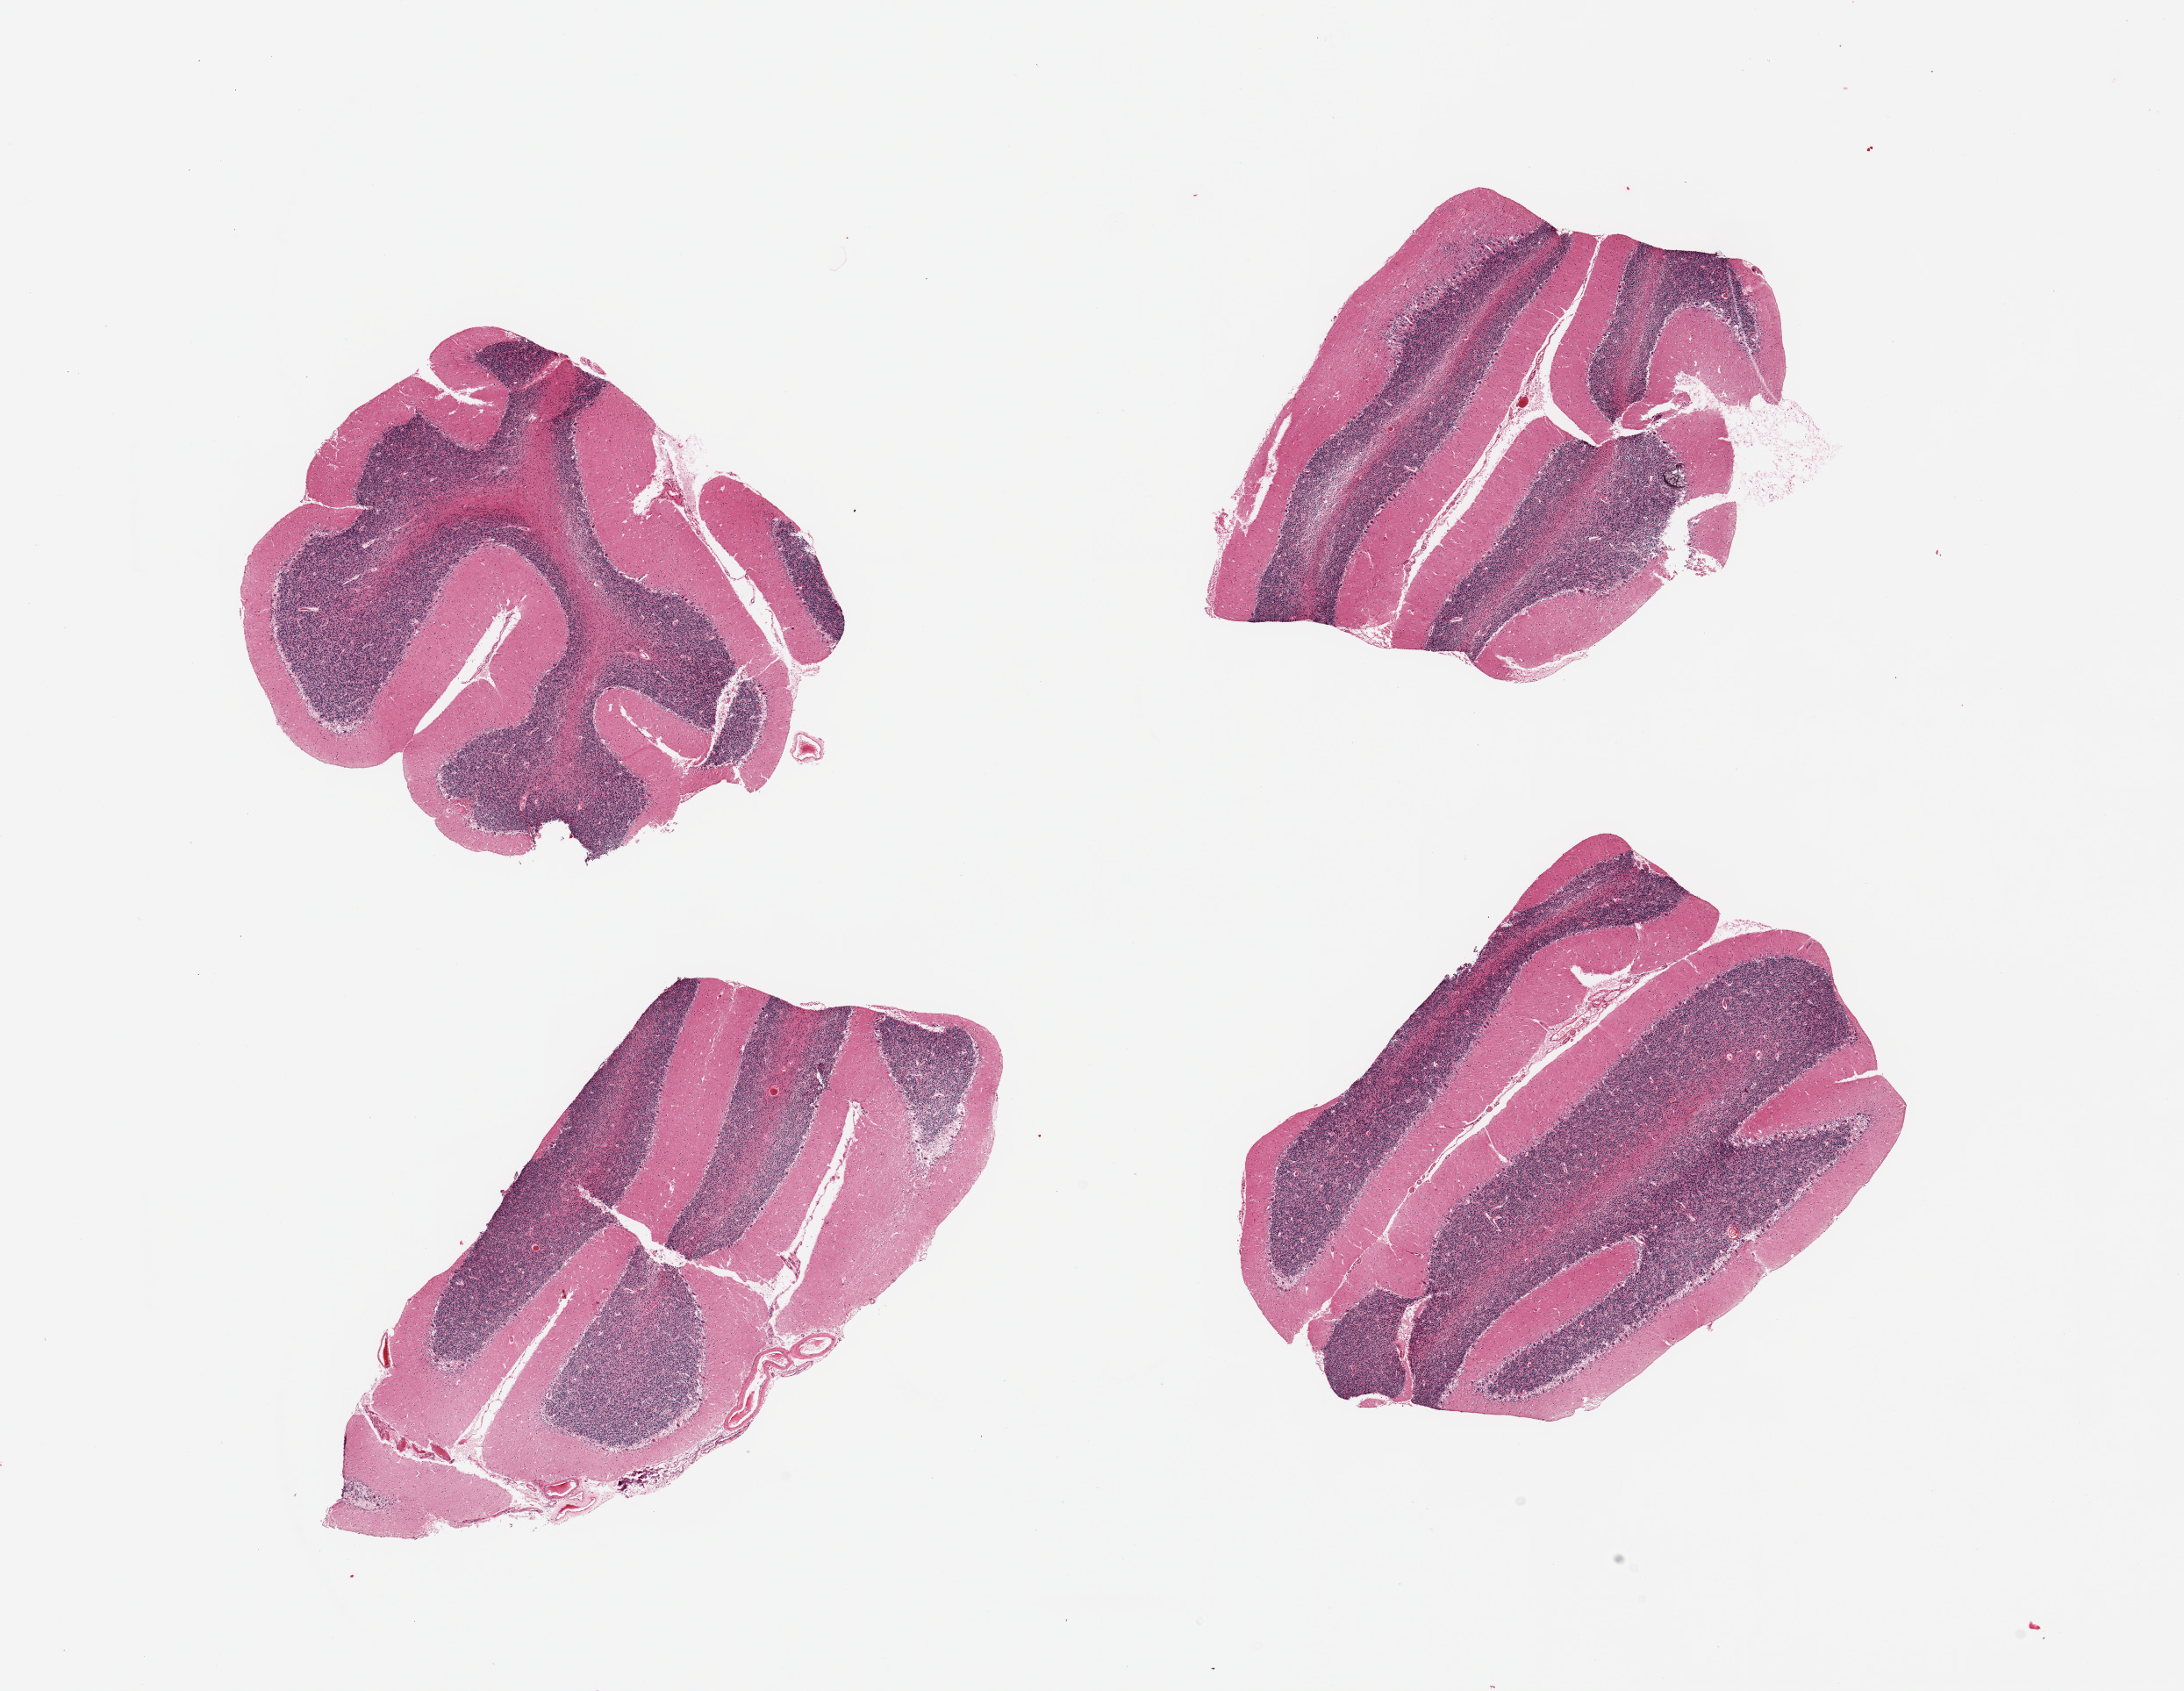
Hematoxylin and eosin (H&E) whole-slide image, brightfield — low-resolution overview of the scanned area, about 19.7 x 15.2 mm. PAXgene-fixed paraffin-embedded (PFPE) section. Section of cerebellum (target tissue). Tissue donor sample. Donor sex: male.
Pathologist's review note for this sample: 4 pieces, no abnormalities.